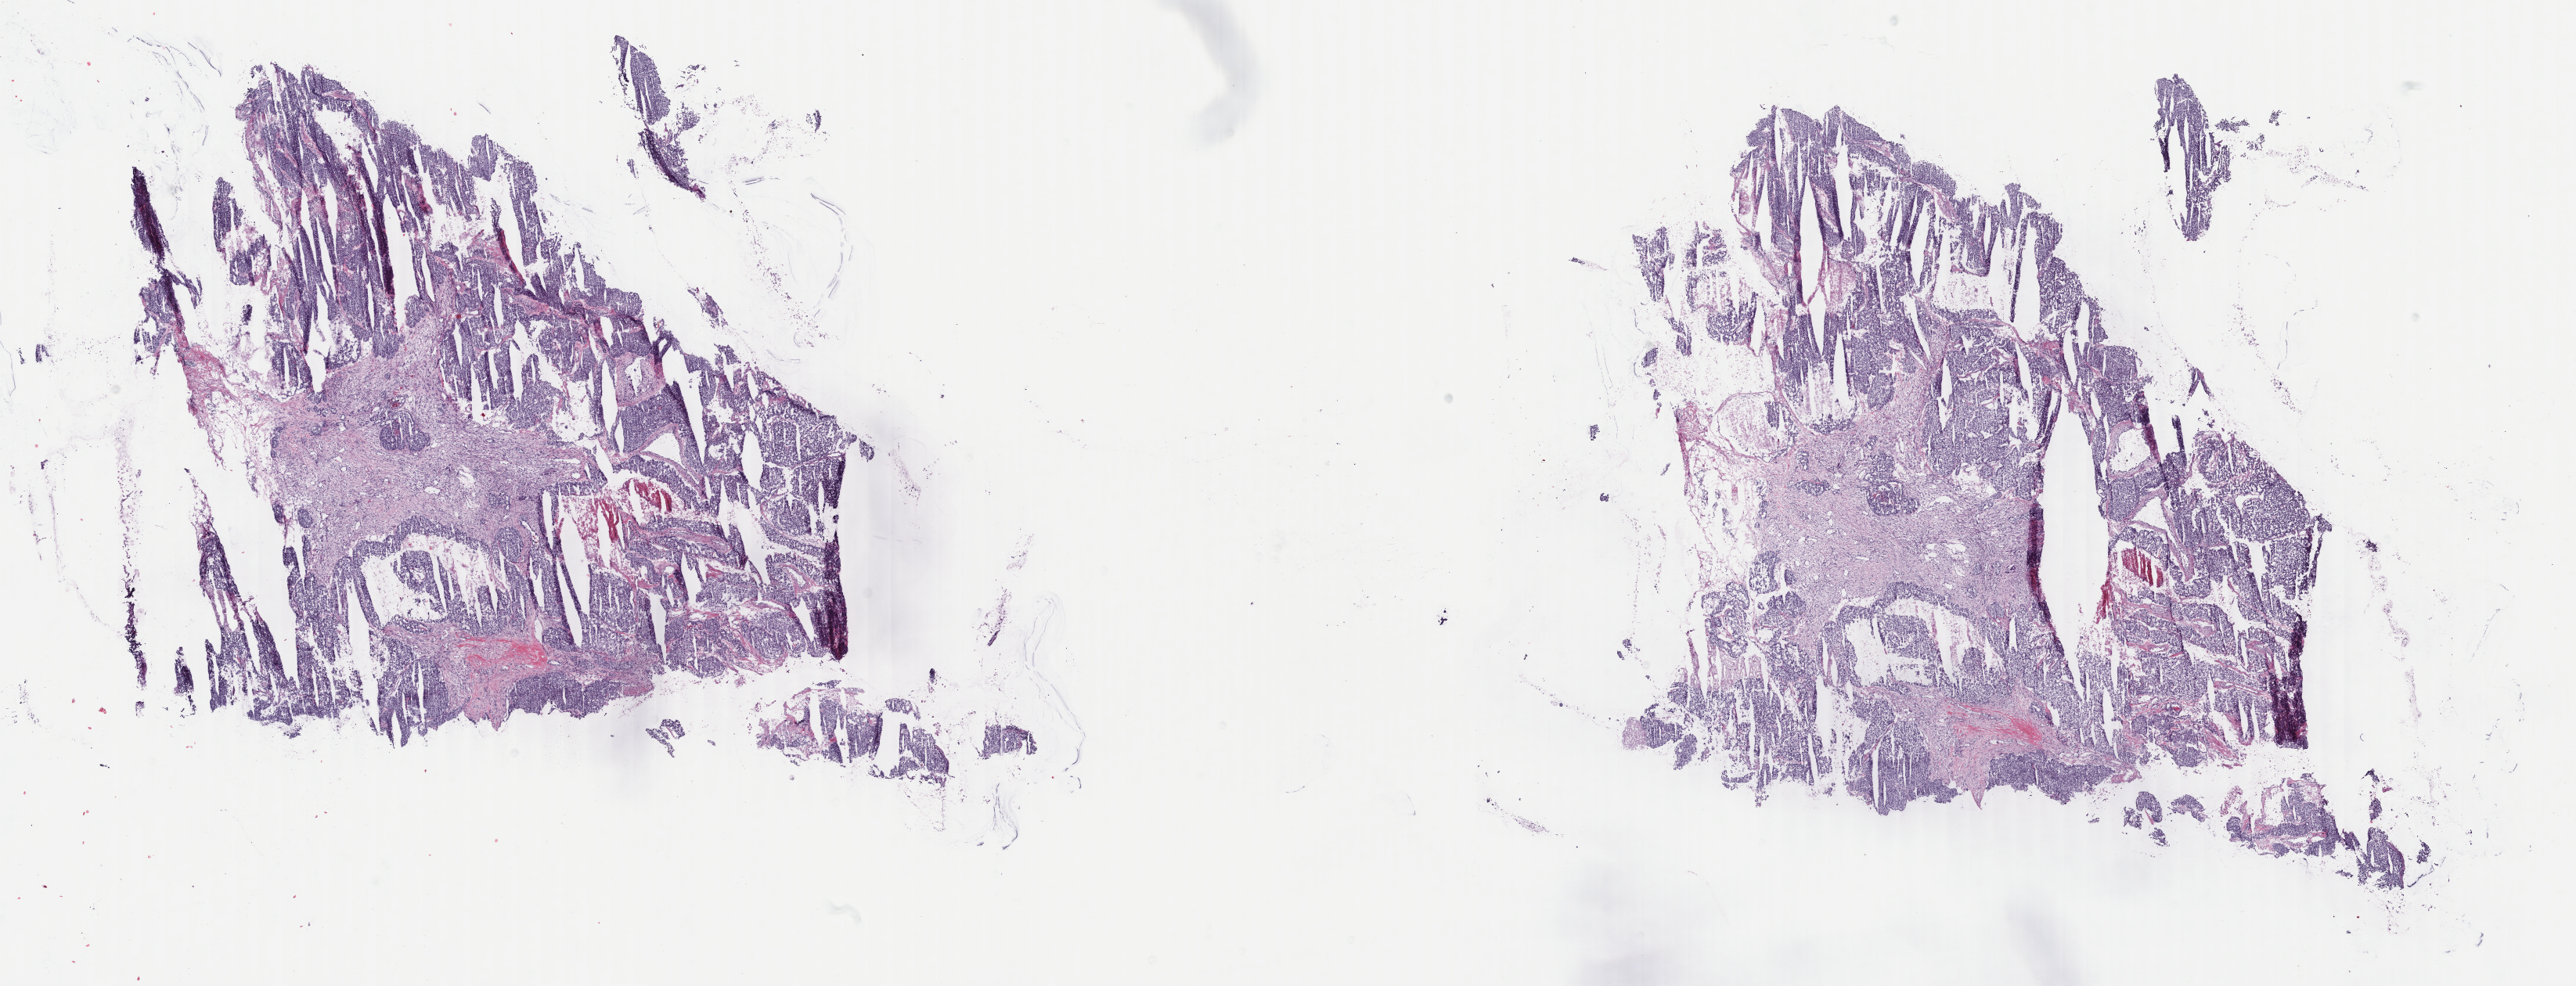
Digitized H&E tissue section (whole slide) — shown as a low-resolution overview of the whole scanned area (about 26.2 x 10.0 mm, slide scanned at 40x). Frozen section. Breast, primary tumour sample. Patient: female, age at initial diagnosis 62 years. Composition of this section per pathologist review: tumour cells 70%, tumour nuclei 75%, normal cells 3%, stromal cells 23%, necrosis 4%. Inflammatory infiltration, as recorded: lymphocyte infiltration 1%, monocyte infiltration 0%, neutrophil infiltration 0%.
Histologic diagnosis: Infiltrating duct carcinoma, NOS. AJCC pathologic stage: IIA. TNM: T2 N0 M0.